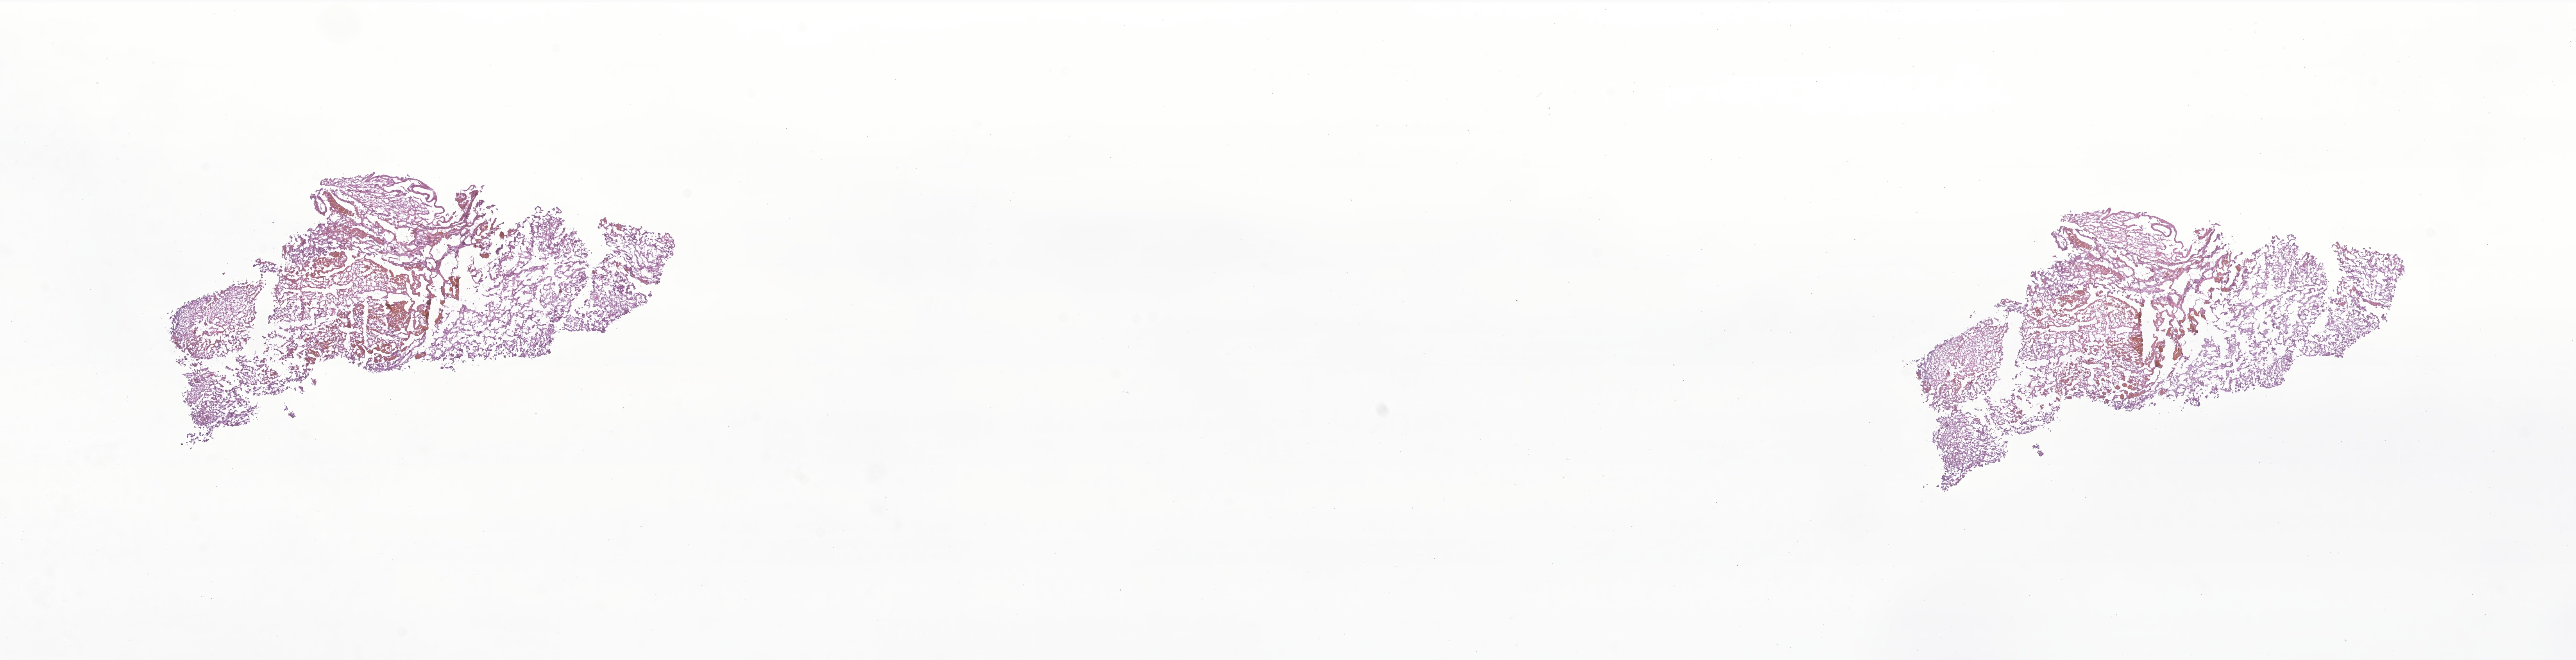
Hematoxylin and eosin (H&E) whole-slide image of tumor tissue from the brain — shown as a low-resolution overview of the whole scanned area (about 27.8 x 7.1 mm); frozen section. Female patient, age 774 days (about 2.1 years).
Diagnosis: Pilocytic astrocytoma.